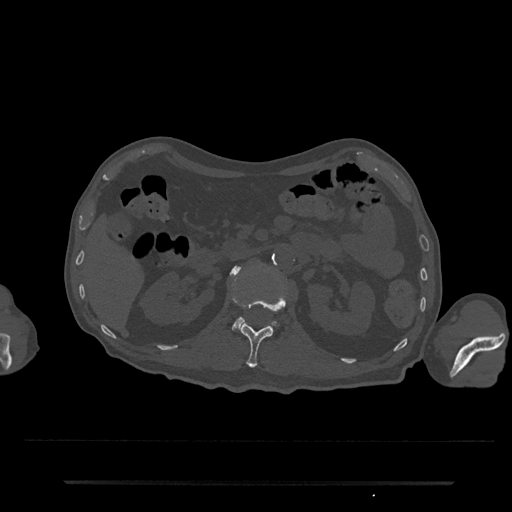
CT including the spine, one axial slice. Position 107 of 797 along the scan axis. 120 kVp. Bone window (W 1800 / L 400 HU). 0.5 mm slice thickness. 512 × 512 image matrix. Male patient, age 74 years. Case-level facts recorded for this patient, not image findings: primary cancer: prostate.
Structures marked on this image (semi-automatic segmentation, software-assisted and operator-edited):
- L1 vertebra: bounding box (x1, y1, x2, y2) in pixels: (232, 292, 287, 368)
- L2 vertebra: (231, 266, 276, 330)